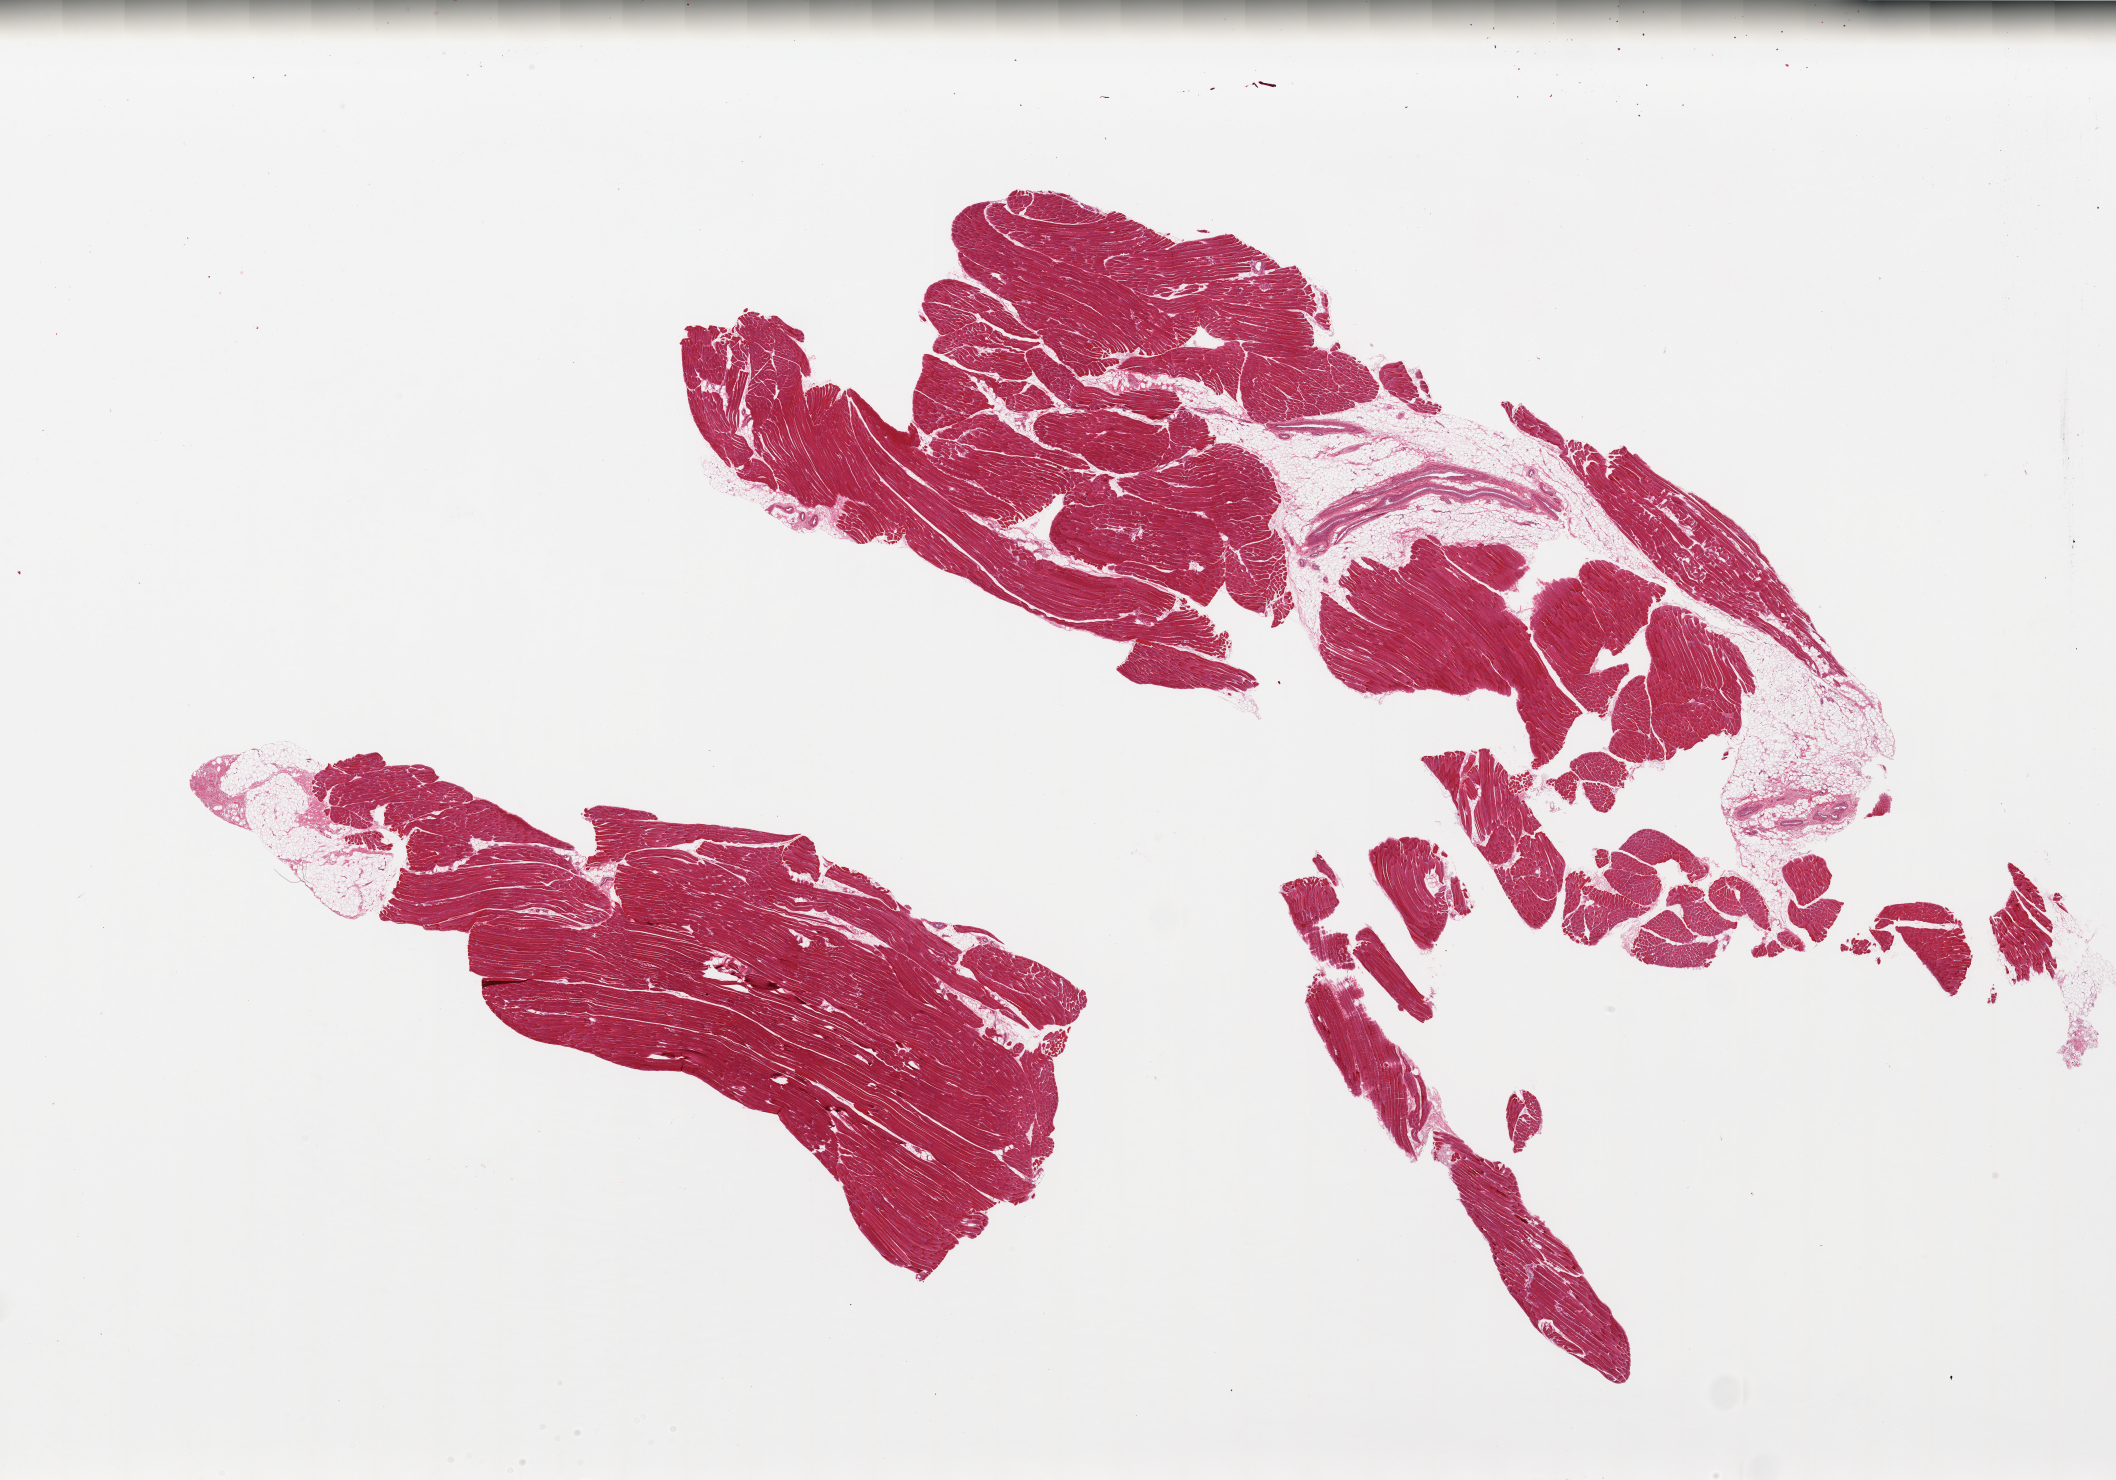
Digitized haematoxylin and eosin-stained section — a low-resolution overview of the entire scanned area, about 33.5 x 23.4 mm; PAXgene-fixed, paraffin-embedded tissue; sampled site (target tissue): skeletal muscle; donor tissue sample. Donor: female.
Reviewer comment on this tissue sample: 2 pieces, ~20% interstitial fat.